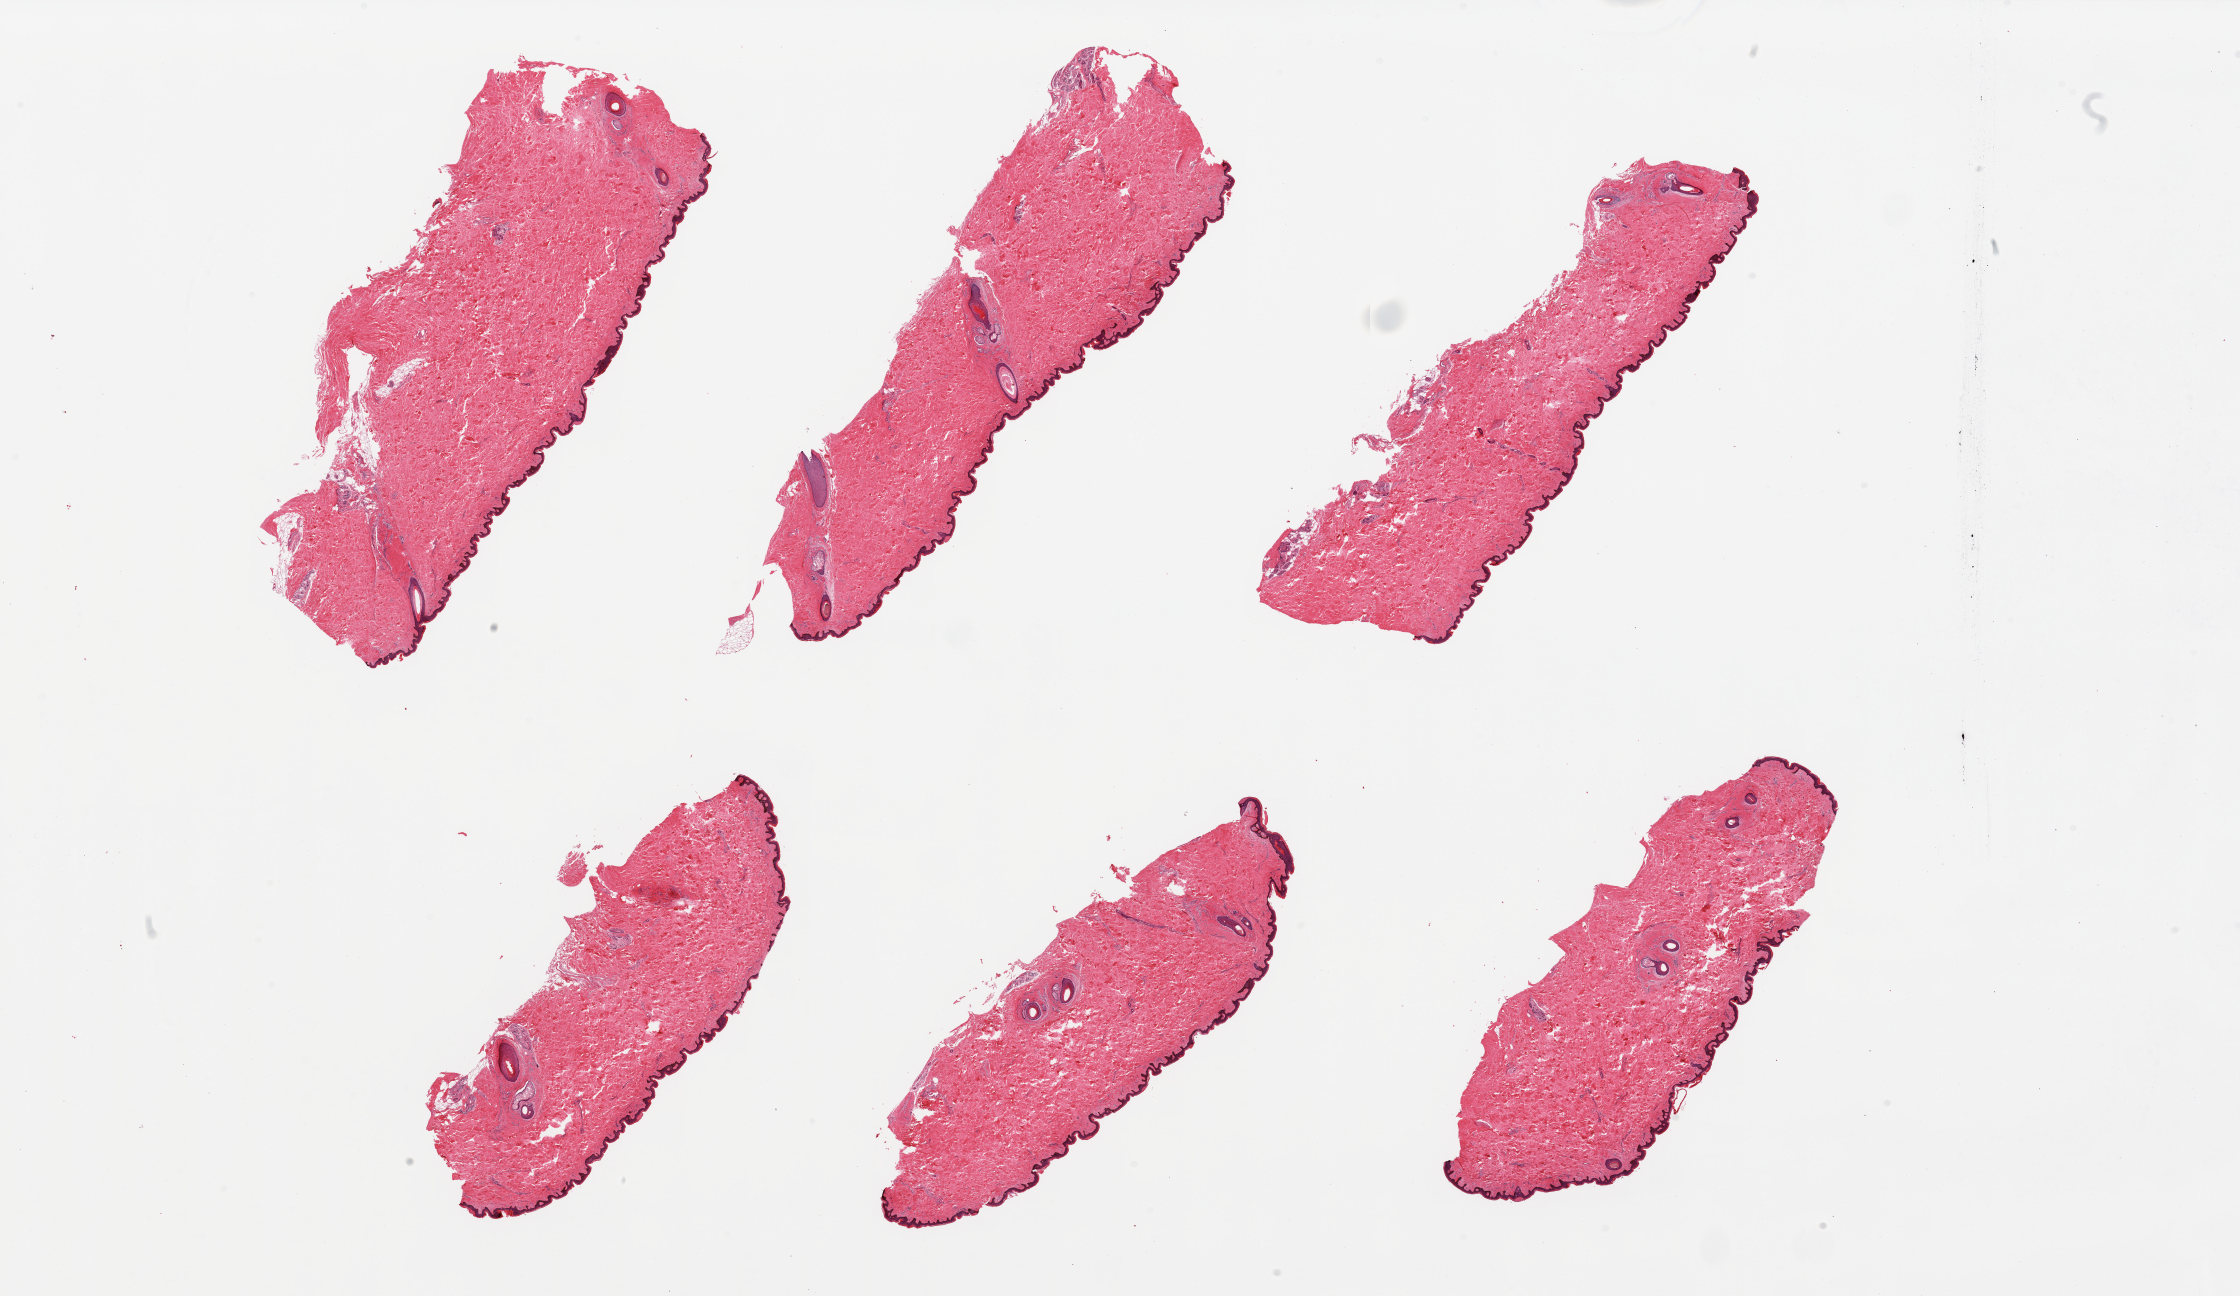
H&E whole-slide image — a low-resolution overview of the entire scanned area, about 35.4 x 20.5 mm, PAXgene-fixed paraffin-embedded (PFPE) section, section of skin of suprapubic region (target tissue), donor tissue sample. Donor sex: male.
* review note (as recorded): 6 pieces, squamous epithelium is ~50-60 microns, minimal dermal fat